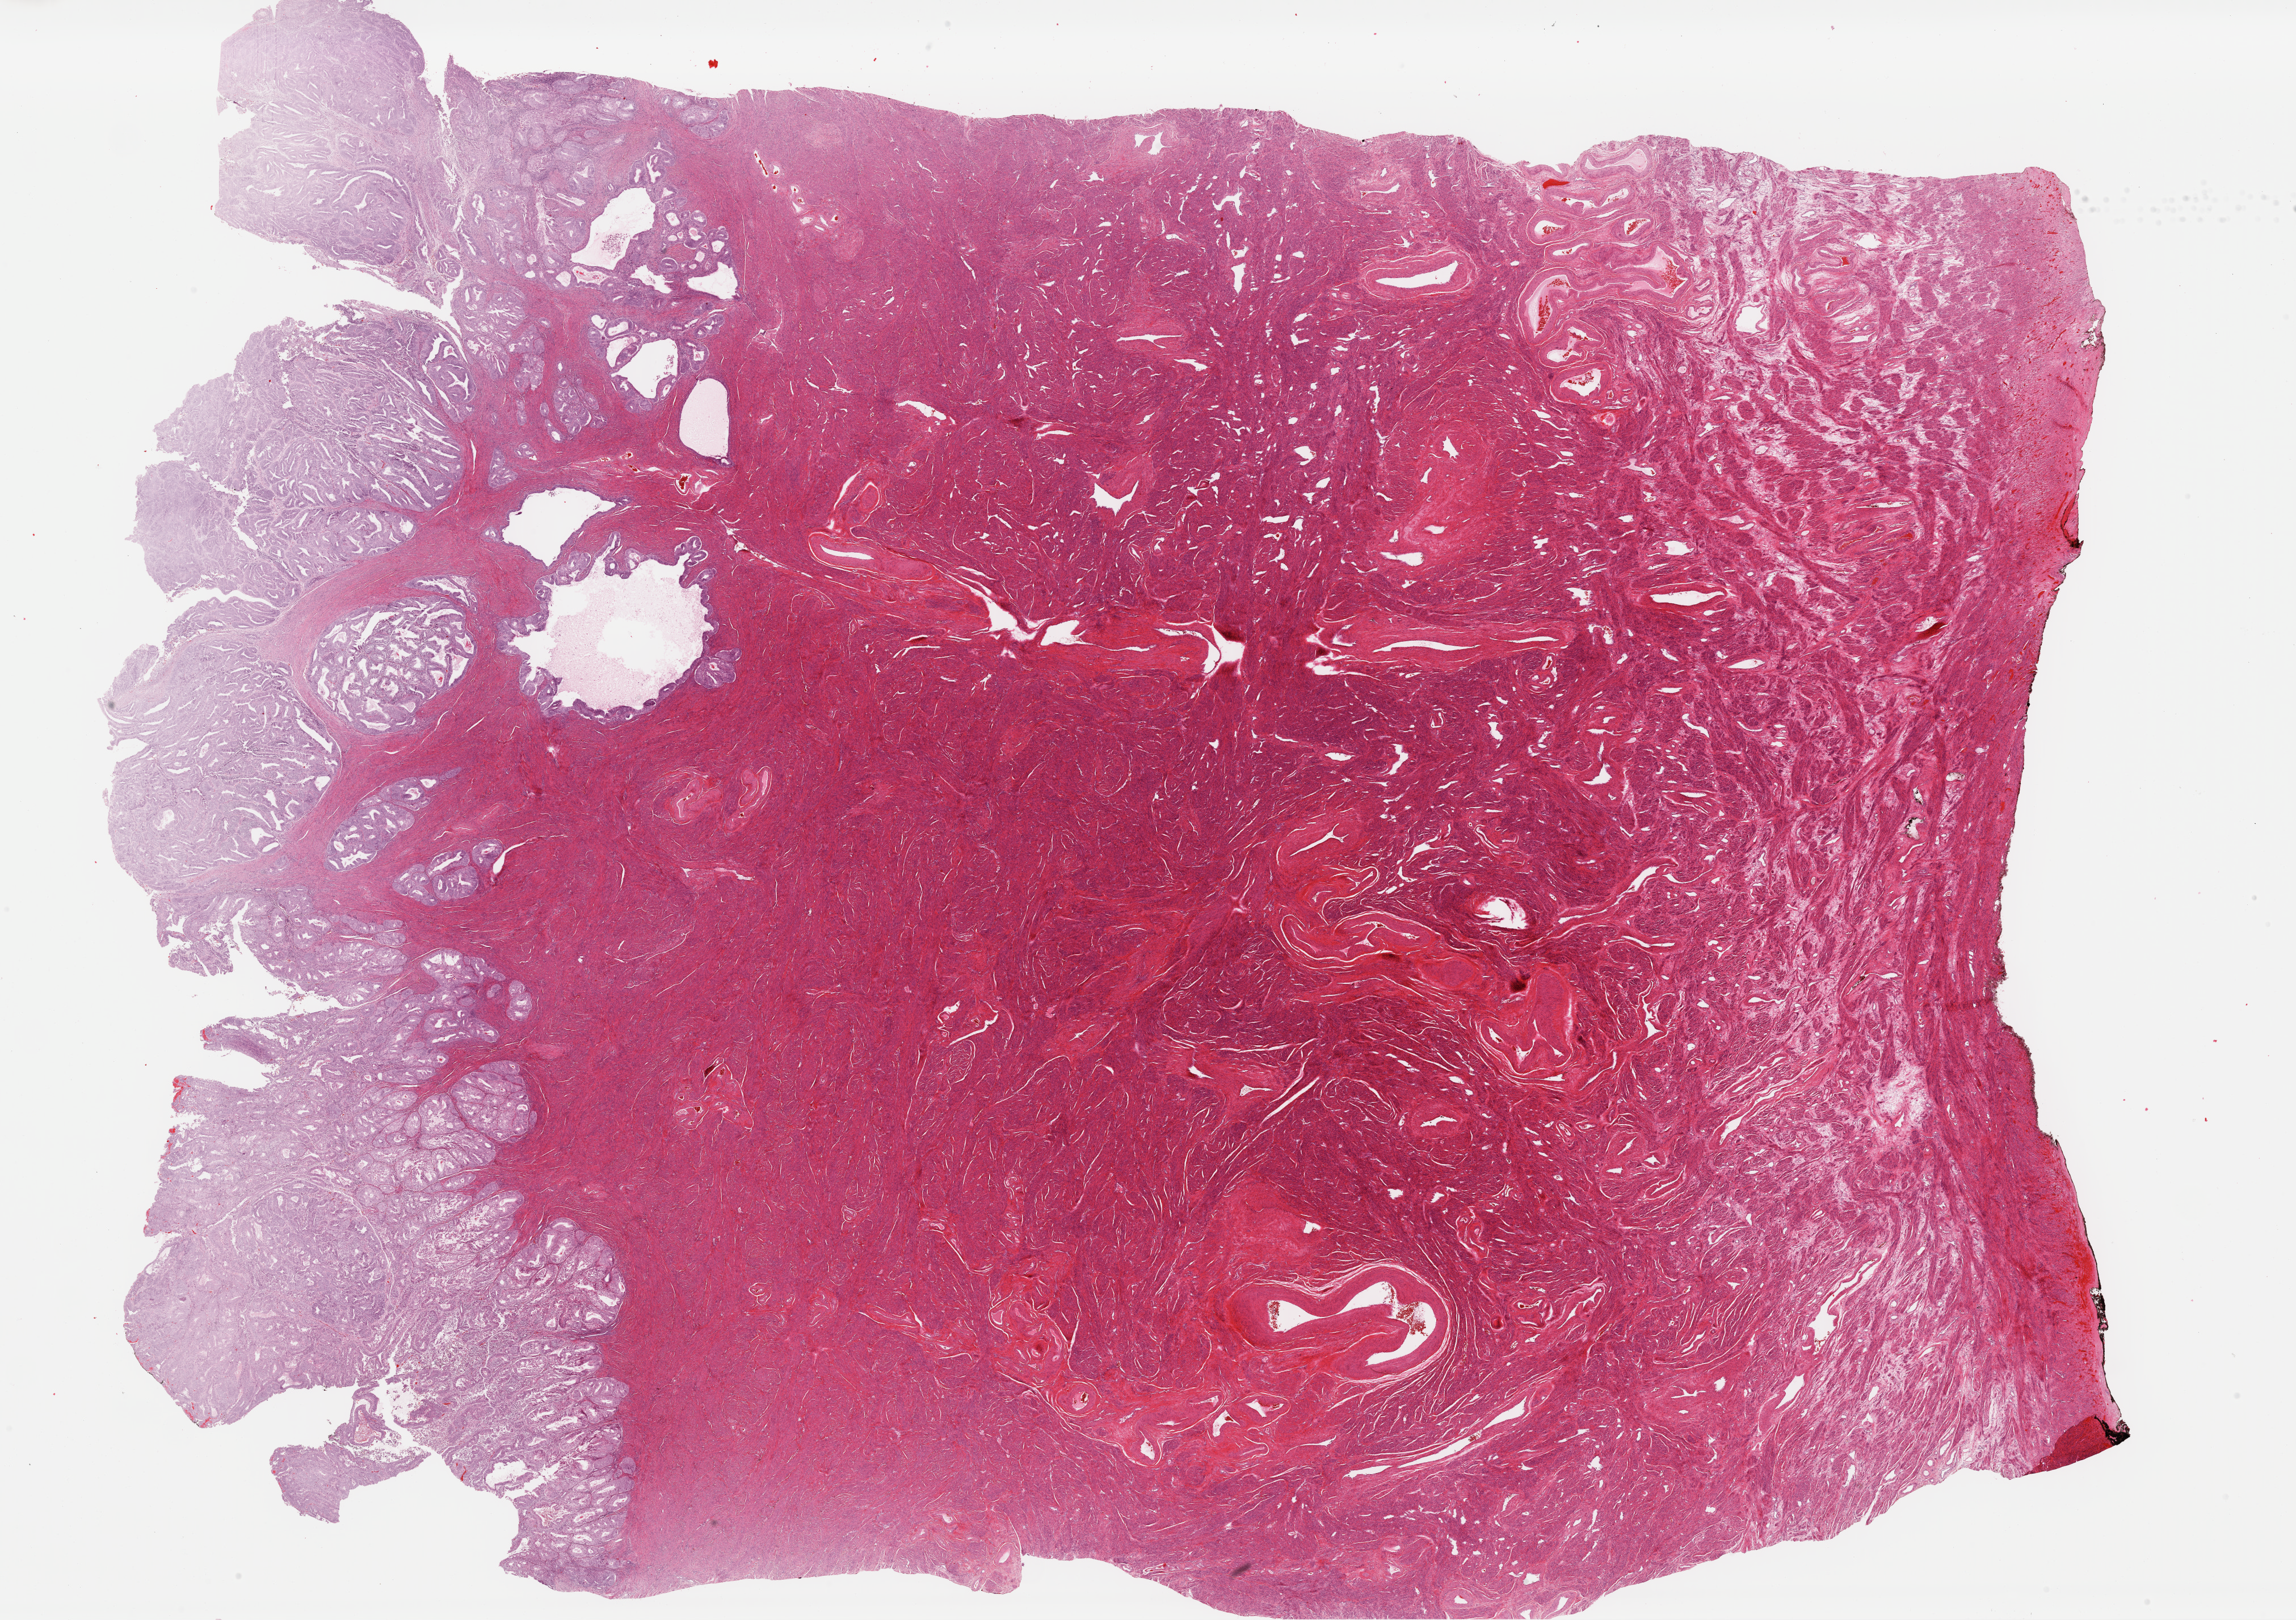
Digitized H&E tissue section (whole slide), whole scanned area (about 32.0 x 22.5 mm) shown as a low-resolution overview, formalin-fixed paraffin-embedded (FFPE) diagnostic section, uterus, primary tumour sample. Female patient; age at initial diagnosis 56 years. Histologic grade: G1 (well differentiated).
Pathologic diagnosis: Endometrioid adenocarcinoma, NOS (endometrium). FIGO stage: IB. Lymph nodes positive (case pathology): 0 of 12 examined.